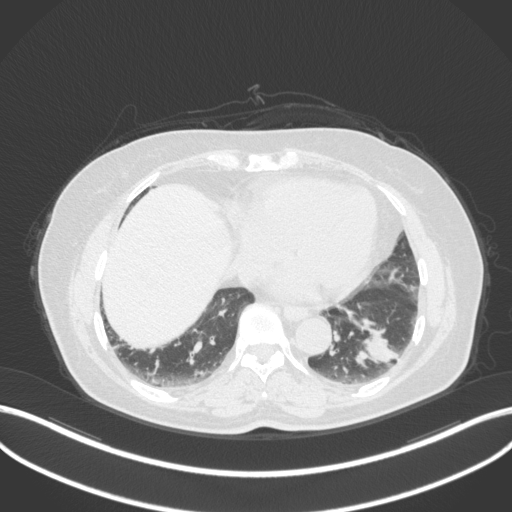
Chest CT, one axial slice. Reconstruction kernel B31f. 120 kVp. Lung window (W 1500 / L -600 HU). 1 mm slice thickness. 512 × 512 image matrix. Patient: female, 59 years. Case-level facts recorded for this patient, not image findings: clinical TNM (as recorded): T2a N0 M0; histopathological grade: G2-3.
Outlined on this slice (rectangle marked by the reading radiologist):
- lung tumour (recorded histology: adenocarcinoma): bounding box (x1, y1, x2, y2) in pixels: (356, 319, 399, 373)